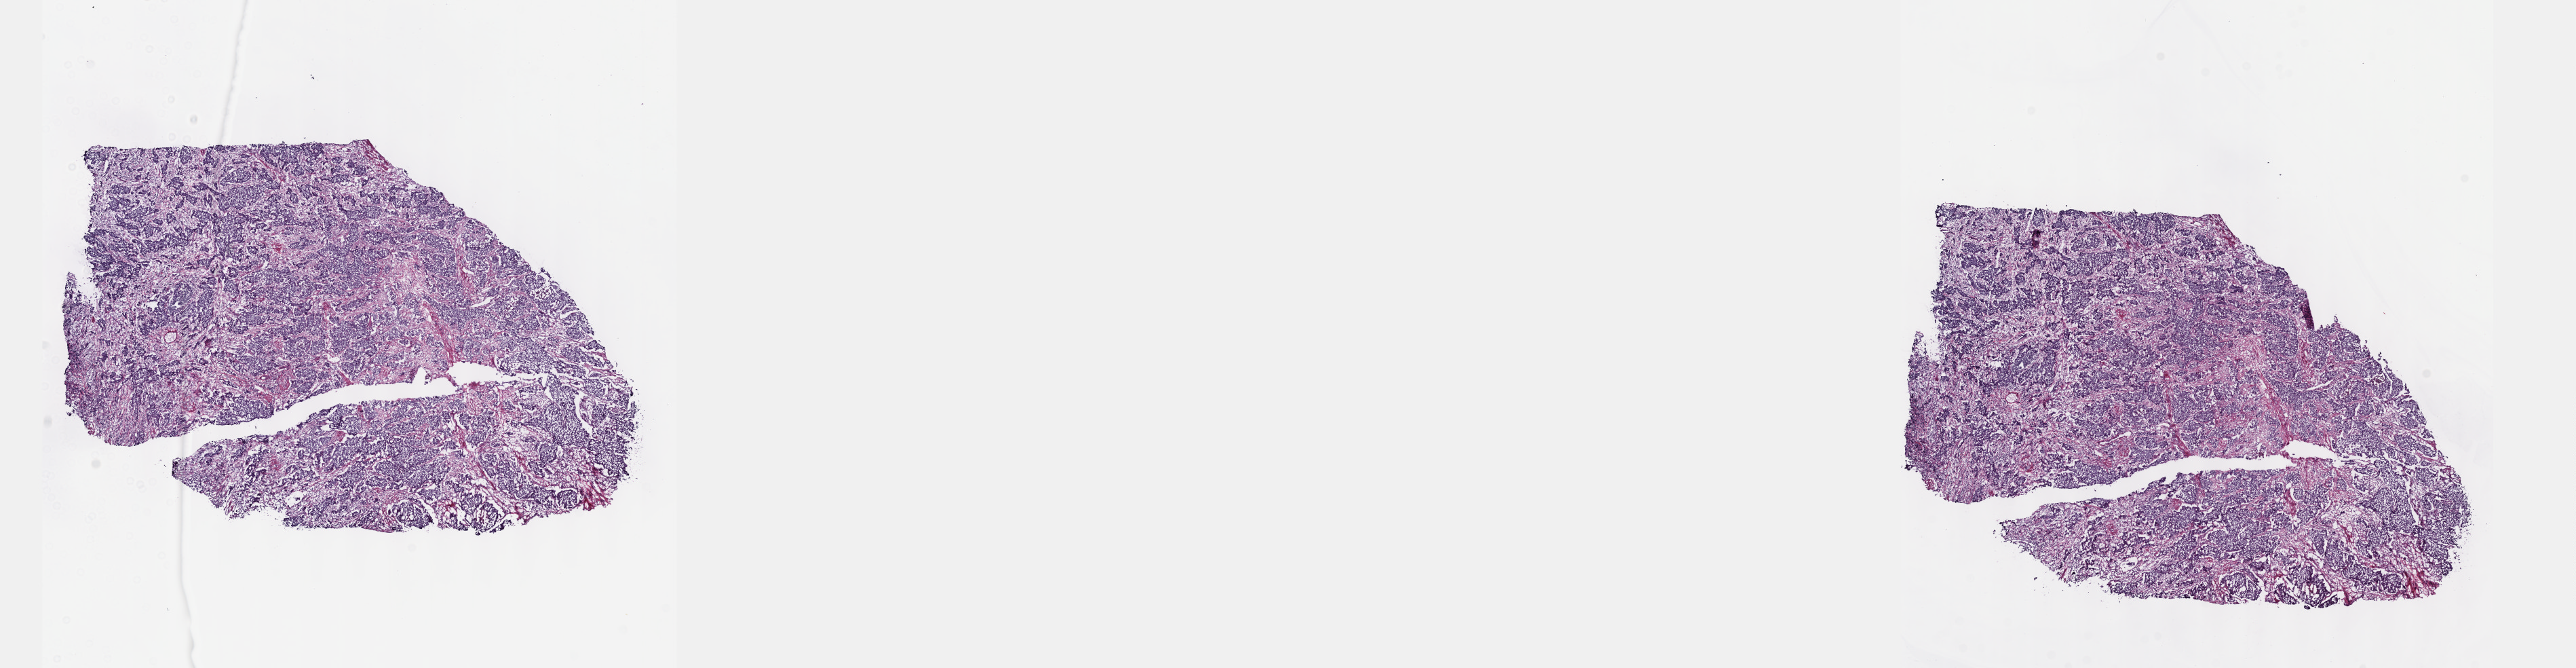
Whole-slide histology image, Hematoxylin and eosin (H&E) stained — a low-resolution overview of the entire scanned area, about 30.7 x 8.0 mm, frozen section from the top of the tissue portion, sample: primary tumour, bladder. Male patient; age at initial diagnosis 64 years. Histologic grade: high grade. Slide review estimates, as recorded: tumour cells 100%, tumour nuclei 75%, normal cells 0%, stromal cells 0%, necrosis 0%. Inflammatory infiltration, as recorded: lymphocyte infiltration 2%, monocyte infiltration 0%, neutrophil infiltration 0%.
Lymph nodes positive (case pathology): 0 of 2 examined. Histologic diagnosis: Transitional cell carcinoma. AJCC pathologic stage: III (7th edition).